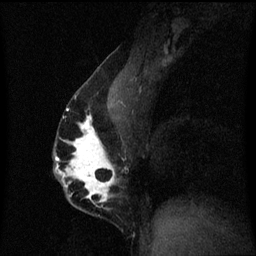
Breast MRI (dynamic contrast-enhanced), one sagittal slice; dynamic contrast-enhanced series, image 2 of 3 at this slice position (ordered by acquisition); 1.5 T; TE 4.2 ms, TR 8.4 ms; 2 mm slice thickness; 256 × 256 image matrix, field of view 200 × 200 mm. Female patient, age 40 years.
Annotated regions visible in this slice (semi-automatic segmentation, software-assisted and operator-edited):
- analysis volume of interest (the breast-tissue region the enhancement analysis was run in; not a lesion): bounding box (x1, y1, x2, y2) in pixels: (54, 84, 121, 211)
- tumour enhancement mask (voxels above the 70 % enhancement threshold inside the analysis volume of interest): (56, 108, 116, 207)